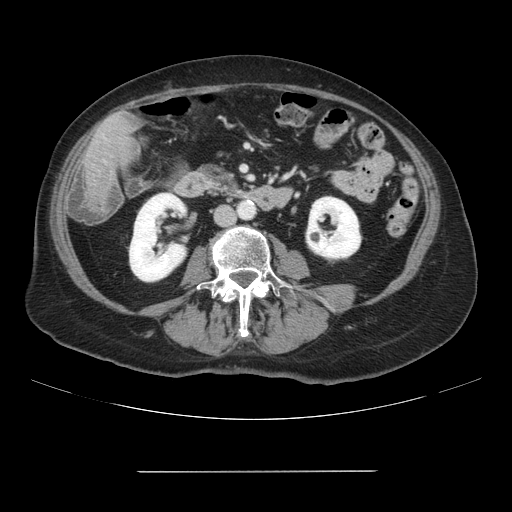
Contrast-enhanced abdominal CT, one axial slice. 120 kVp. Intravenous contrast given. Soft-tissue window (W 400 / L 40 HU). 2.5 mm slice thickness. 512 × 512 image matrix, field of view 400 × 400 mm. Female patient, age 74 years. From the clinical record (not read from this slice): diagnosis: colorectal cancer liver metastases, imaged before liver resection; multiple liver metastases: yes.
Annotated regions visible in this slice (expert manual segmentation):
- liver: bounding box (x1, y1, x2, y2) in pixels: (85, 114, 135, 210)